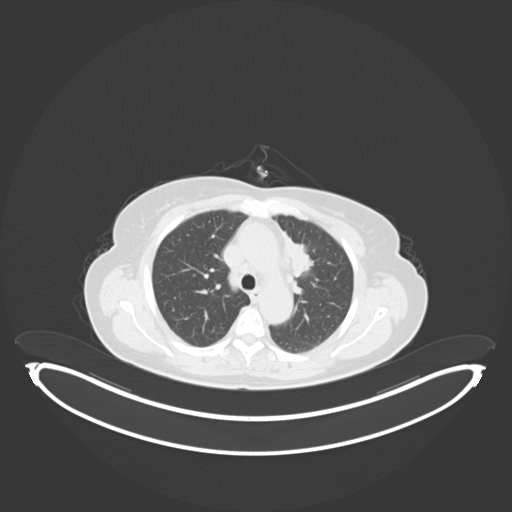
Chest CT, one axial slice; slice 191 of 243 in the series (ordered by position); lung window (W 1500 / L -600 HU); 3 mm slice thickness; 512 × 512 image matrix, field of view 500 × 500 mm. Patient: female, 65 years. Case-level facts recorded for this patient, not image findings: clinical TNM (as recorded): T2a N0 M0; histopathological grade: G2-3.
Annotated regions visible in this slice (bounding box drawn by a radiologist):
- lung tumour (recorded histology: adenocarcinoma): bounding box [x1, y1, x2, y2] px = [282, 232, 315, 277]